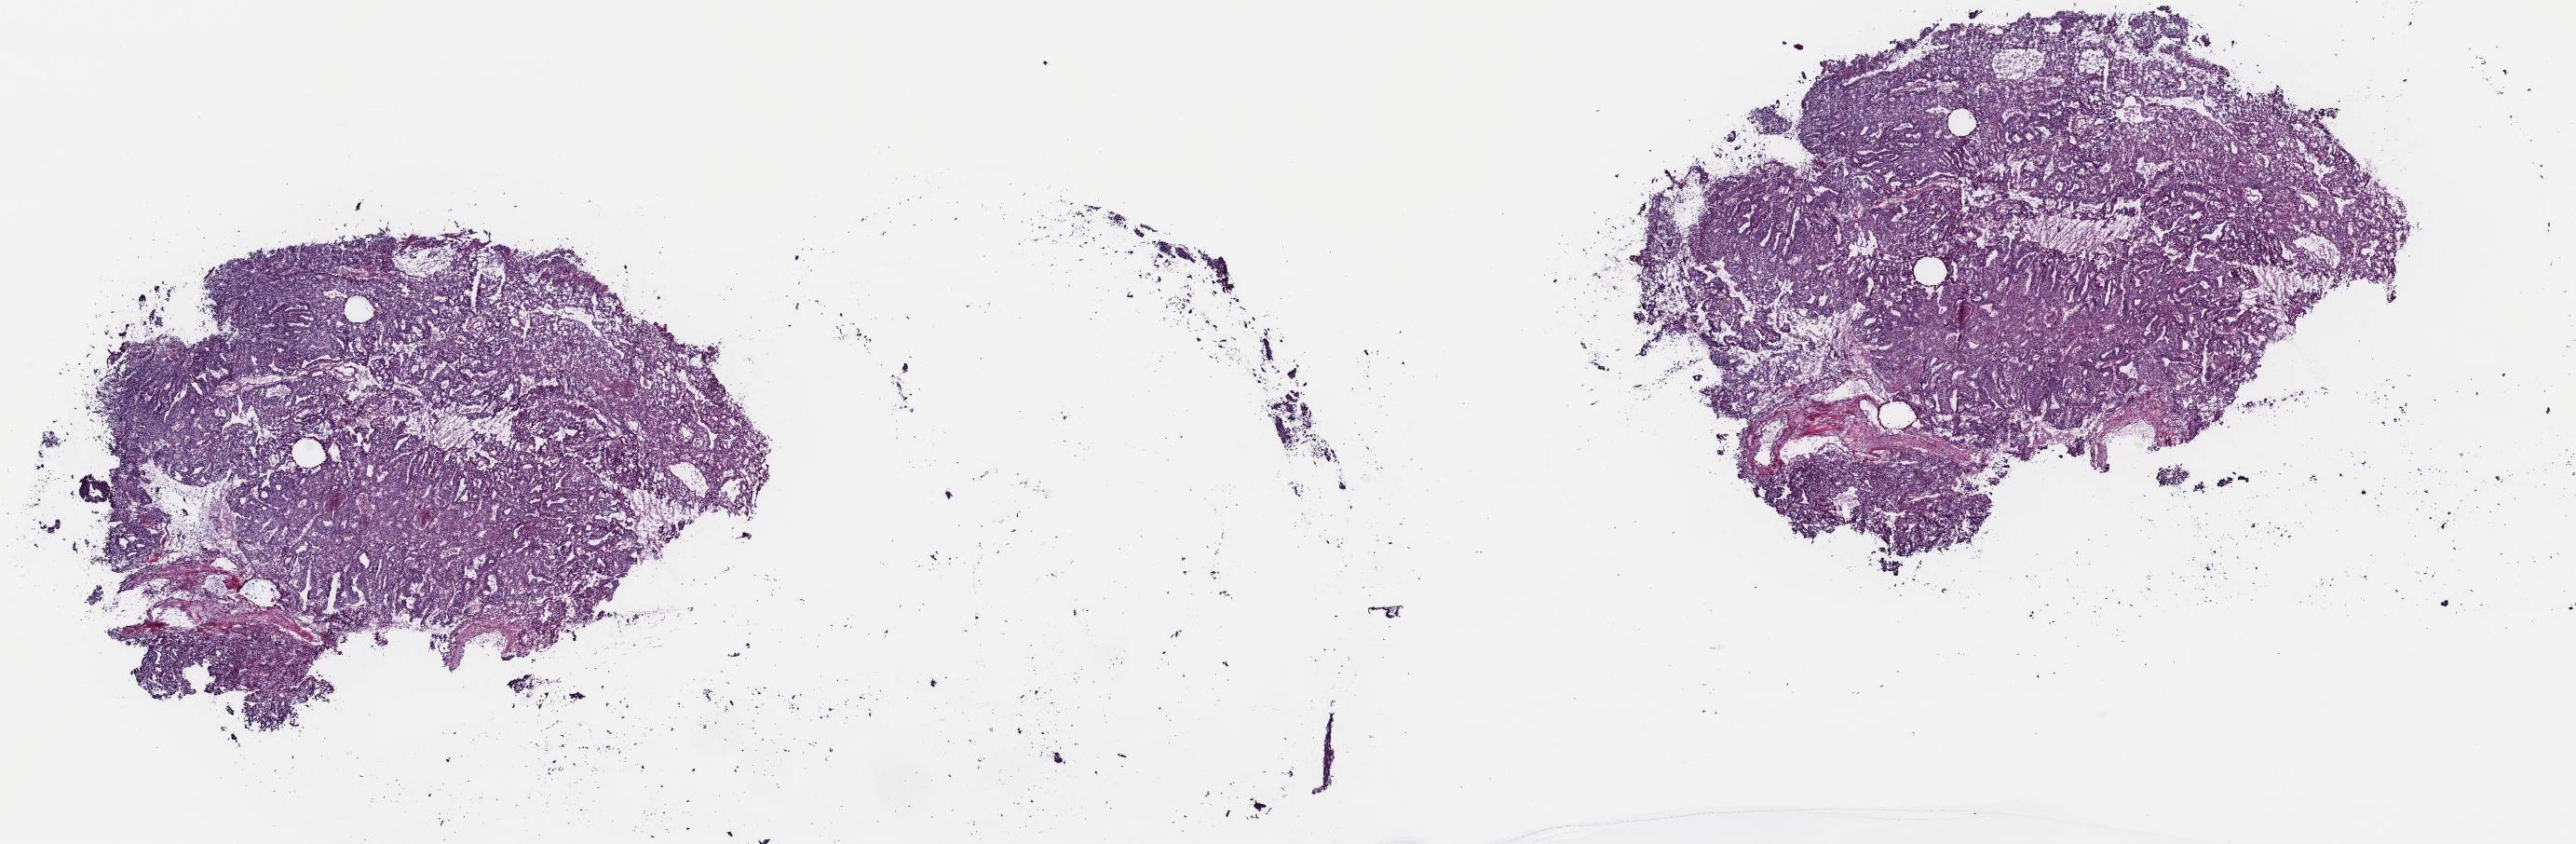
Whole-slide histology image, Hematoxylin and eosin (H&E) stained, low-resolution overview of the scanned area, about 21.9 x 7.2 mm (from a 40x scan), frozen section from the top of the tissue portion, sample: primary tumour, uterus. Female patient; age at initial diagnosis 63 years. Histologic grade: G3 (poorly differentiated). Pathologist review of this section (percent, as recorded): tumour cells 95%, tumour nuclei 95%, normal cells 0%, stromal cells 0%, necrosis 5%. Infiltration values recorded for this section: lymphocyte infiltration 1%, monocyte infiltration 1%, neutrophil infiltration 1%.
- FIGO stage: IA
- diagnosis: Endometrioid adenocarcinoma, NOS (endometrium)